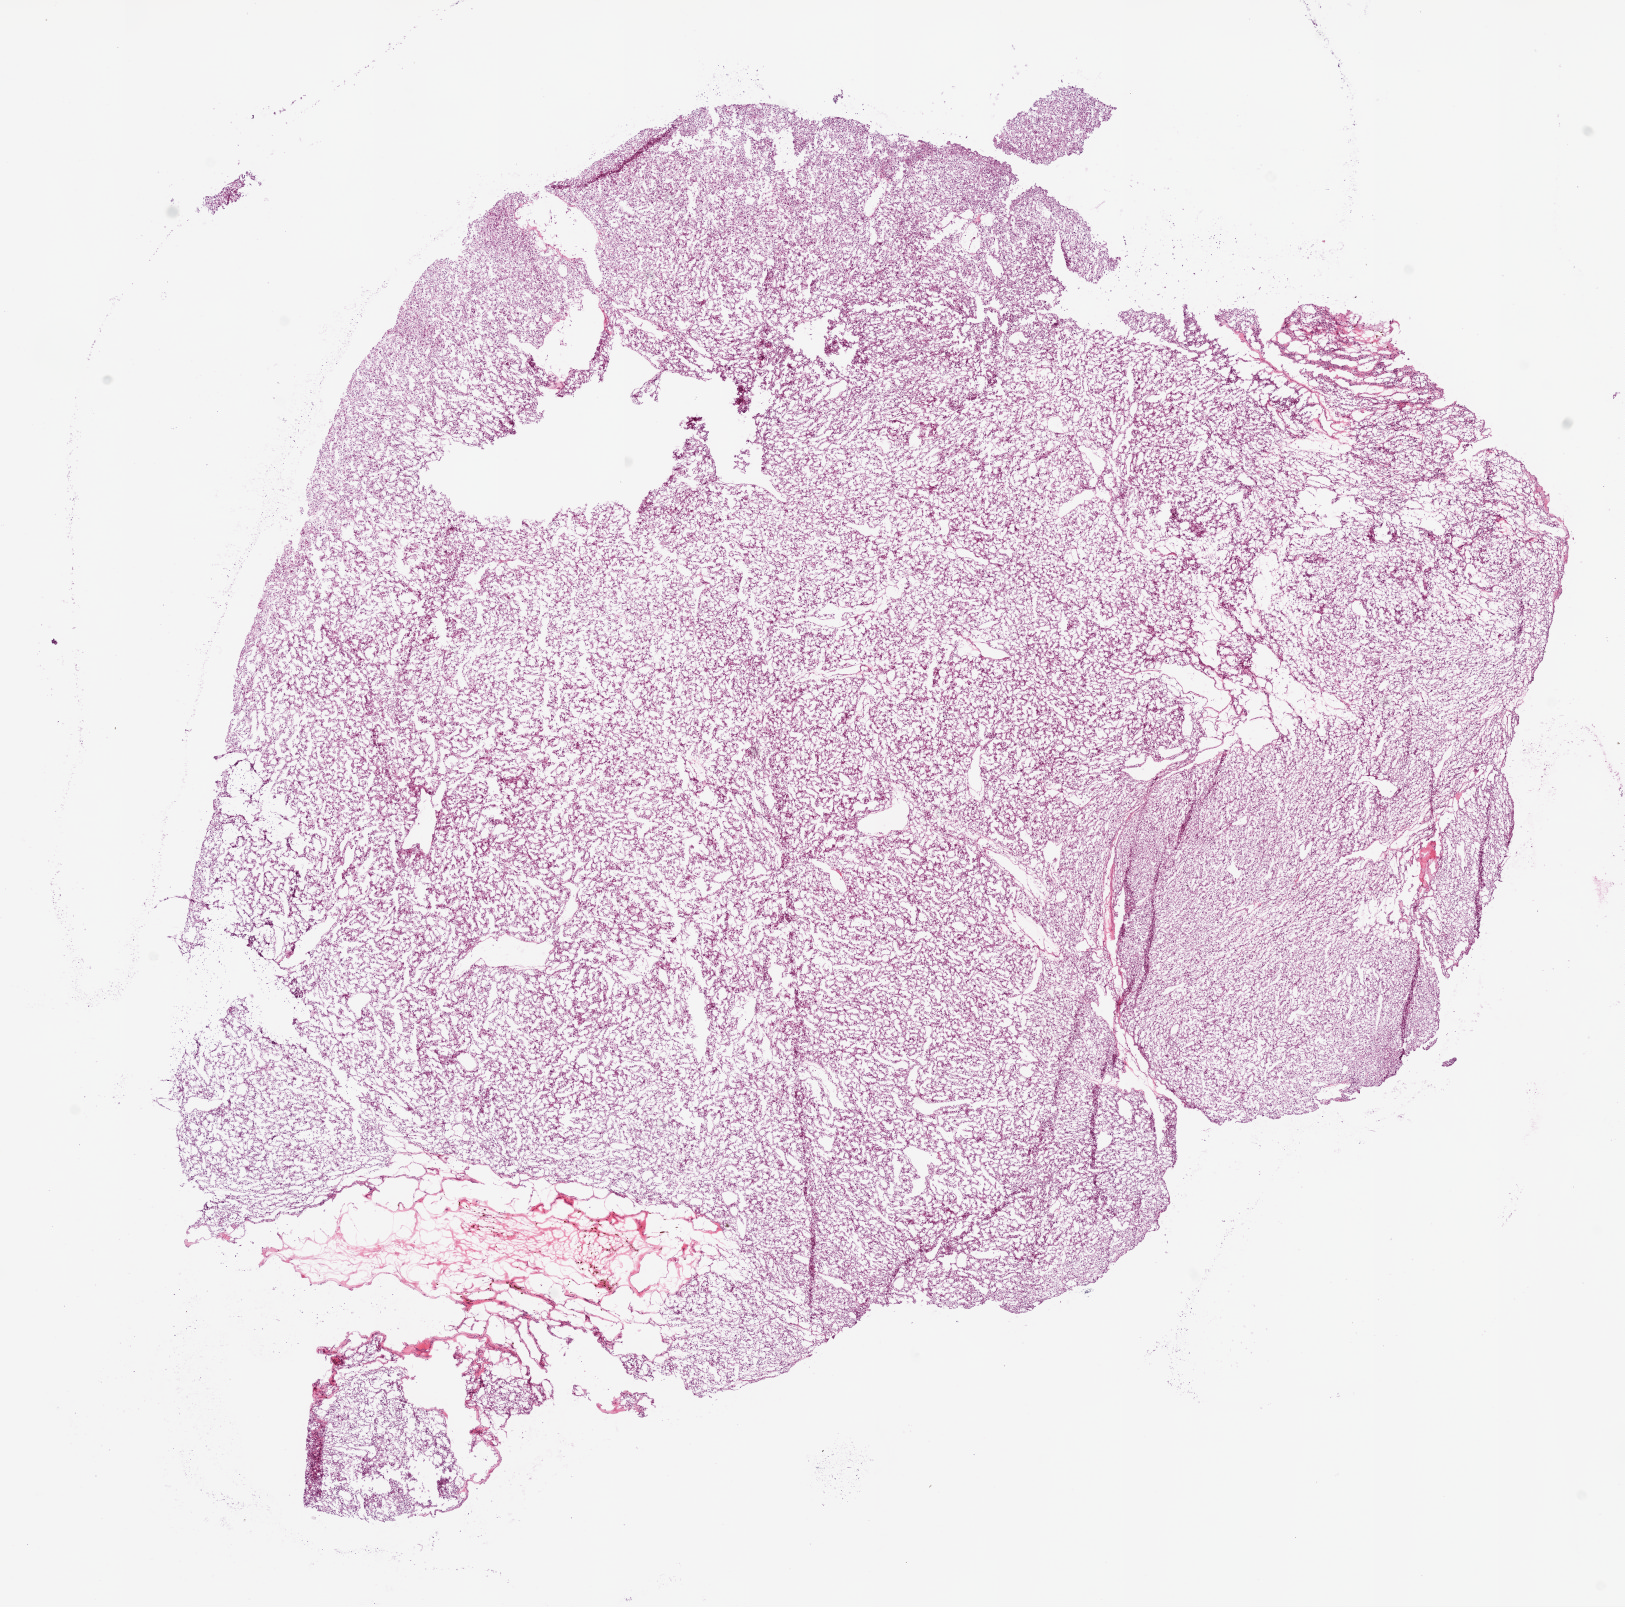
Digitized H&E tissue section (whole slide), shown as a low-resolution overview of the whole scanned area (about 13.0 x 12.9 mm); frozen section; primary tumour sample from the kidney. Male patient; age at initial diagnosis 56 years. Histologic grade: G2 (moderately differentiated). Composition of this section per pathologist review: tumour cells 90%, tumour nuclei 85%, normal cells 0%, stromal cells 10%, necrosis 0%.
- laterality: right
- AJCC pathologic stage: I (7th edition)
- pathologic diagnosis: Clear cell adenocarcinoma, NOS